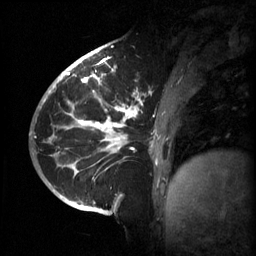
Breast MRI (dynamic contrast-enhanced), one sagittal slice; position 21 of 60 along the scan axis; 3 images stored at this slice position (order not interpretable as contrast timing); 1.5 T; TE 4.2 ms, TR 11 ms; 2 mm slice thickness; 256 × 256 image matrix, field of view 220 × 220 mm. Female patient, age 51 years.
Outlined on this slice (semi-automatic segmentation, software-assisted and operator-edited):
- analysis volume of interest (the breast-tissue region the enhancement analysis was run in; not a lesion): bounding box (x1, y1, x2, y2) in pixels: (63, 80, 187, 201)
- tumour enhancement mask (voxels above the 70 % enhancement threshold inside the analysis volume of interest): (65, 80, 158, 179)